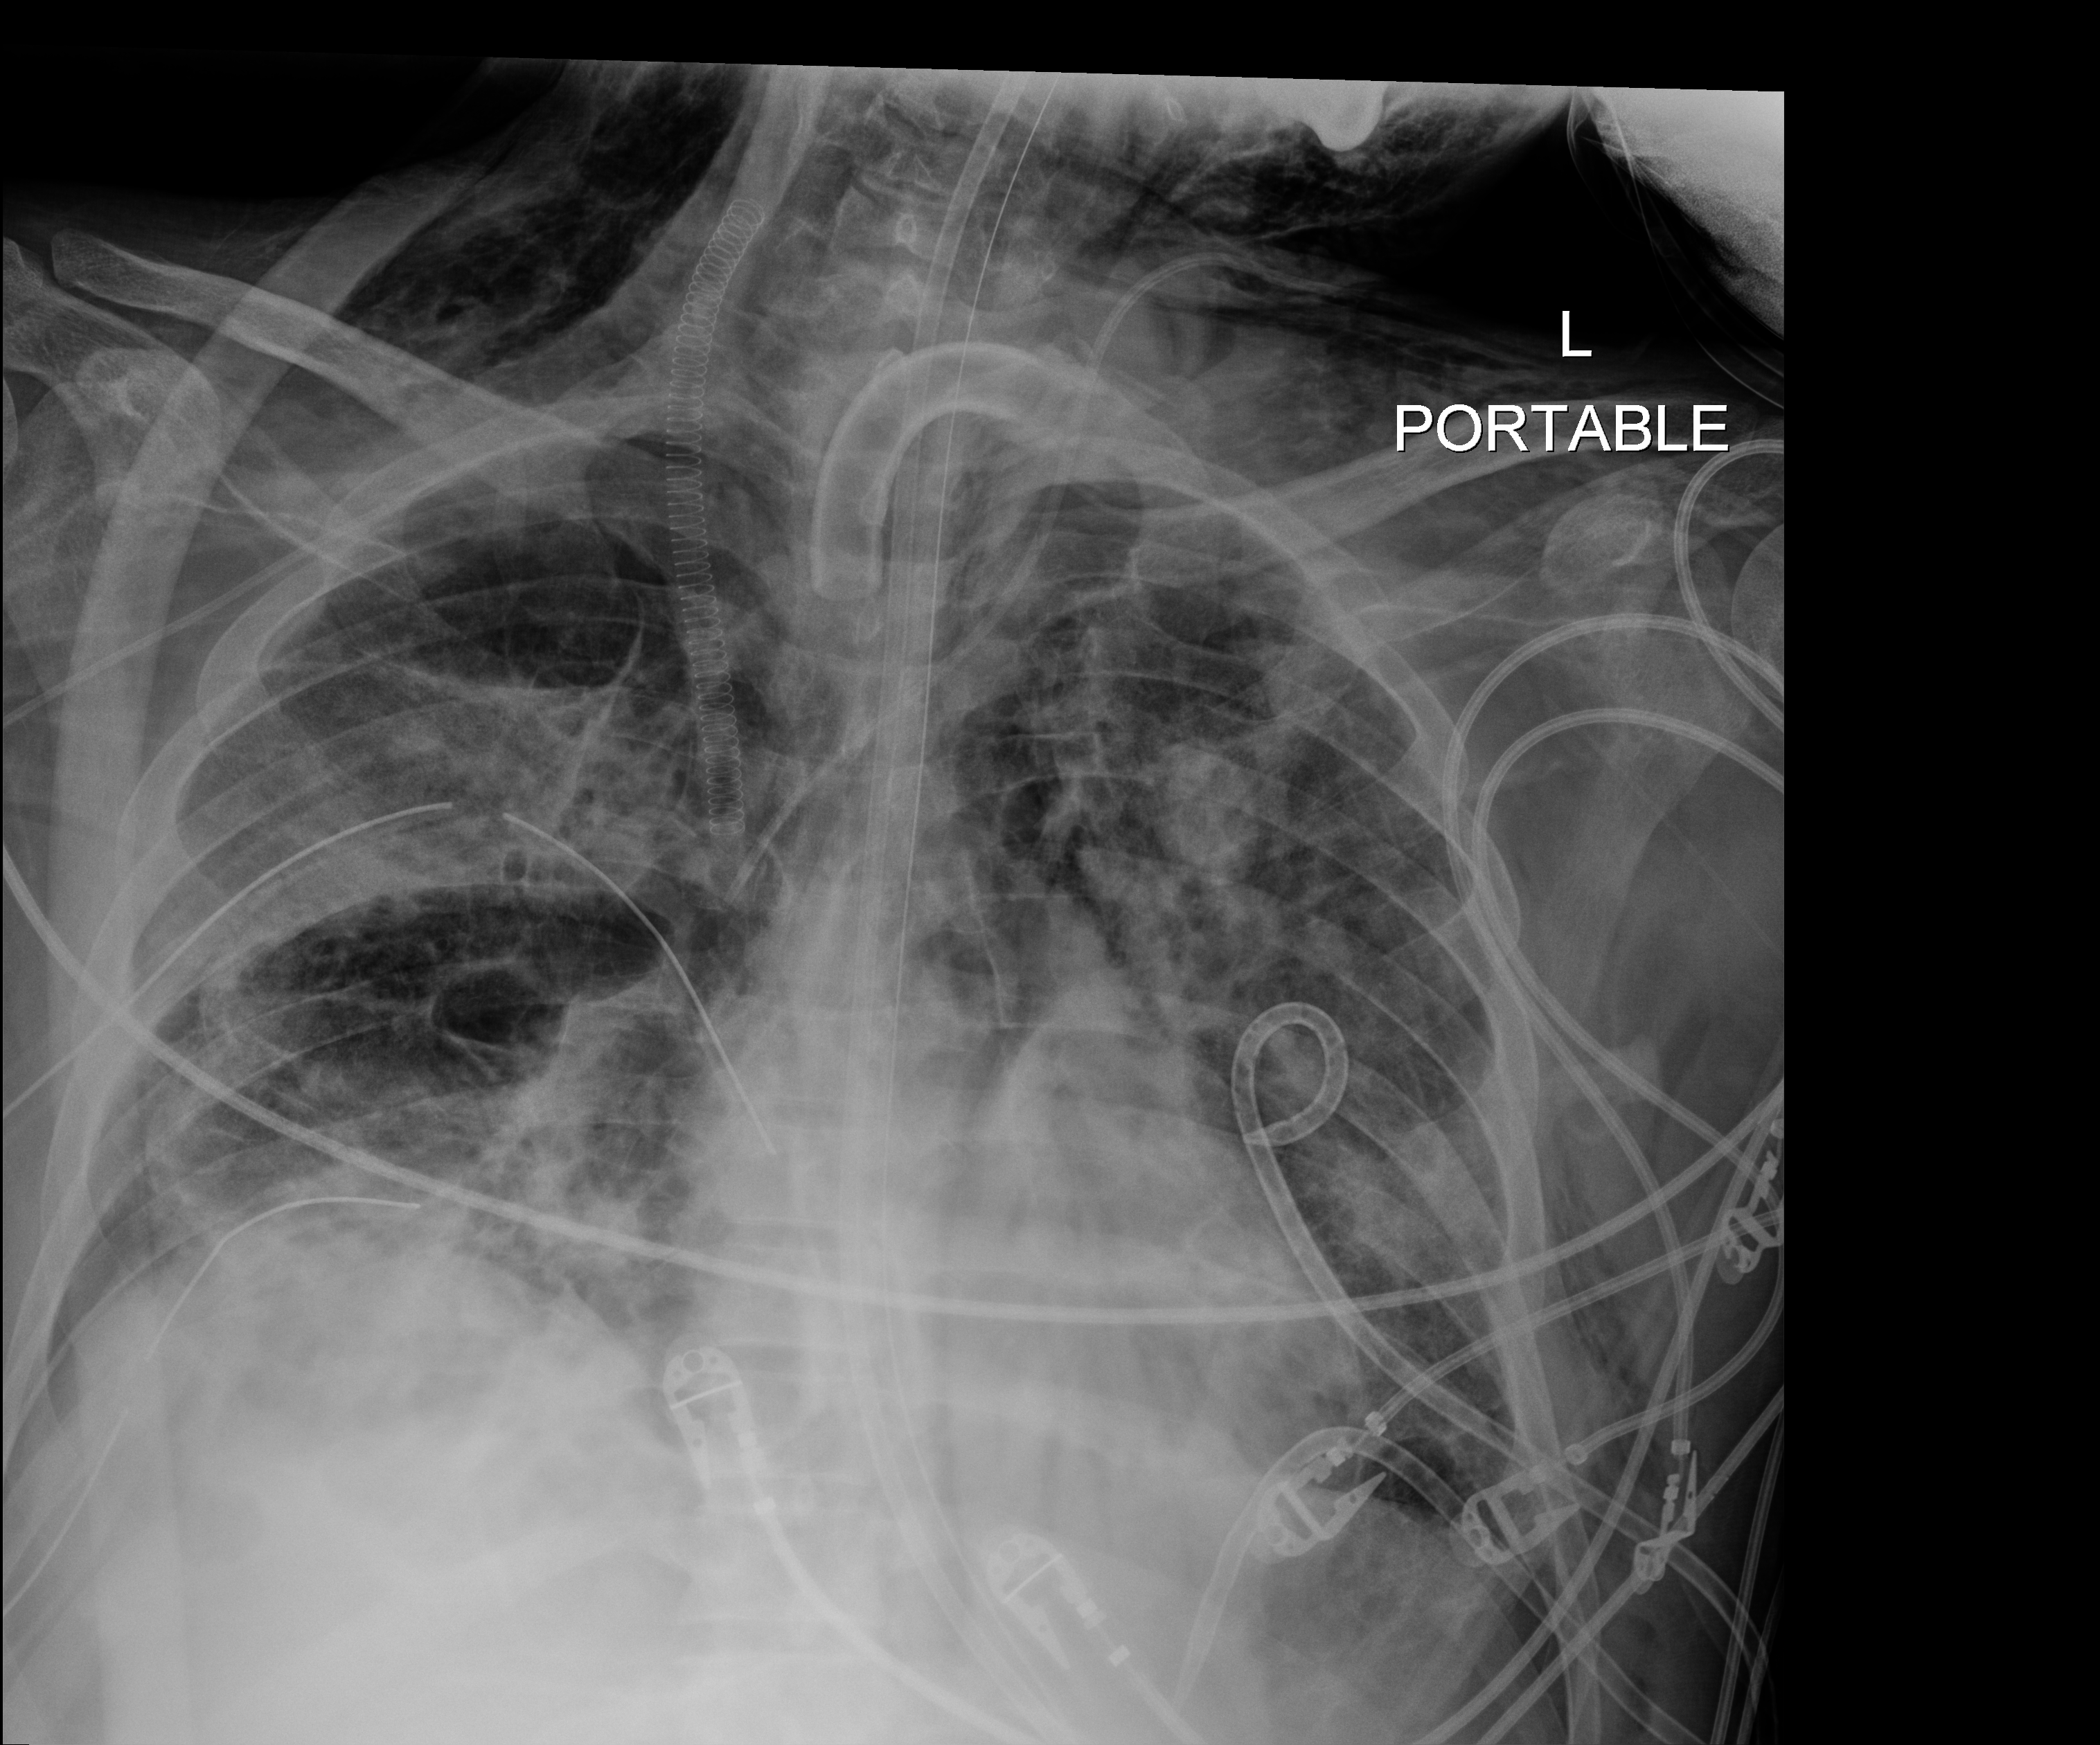
Chest X-ray; anteroposterior (AP) projection. Patient hospitalised with COVID-19, aged 18–59 years.
Hospital-stay facts (about this admission, not read from this image; timing relative to this image not recorded):
- chronic kidney disease (admission record): no